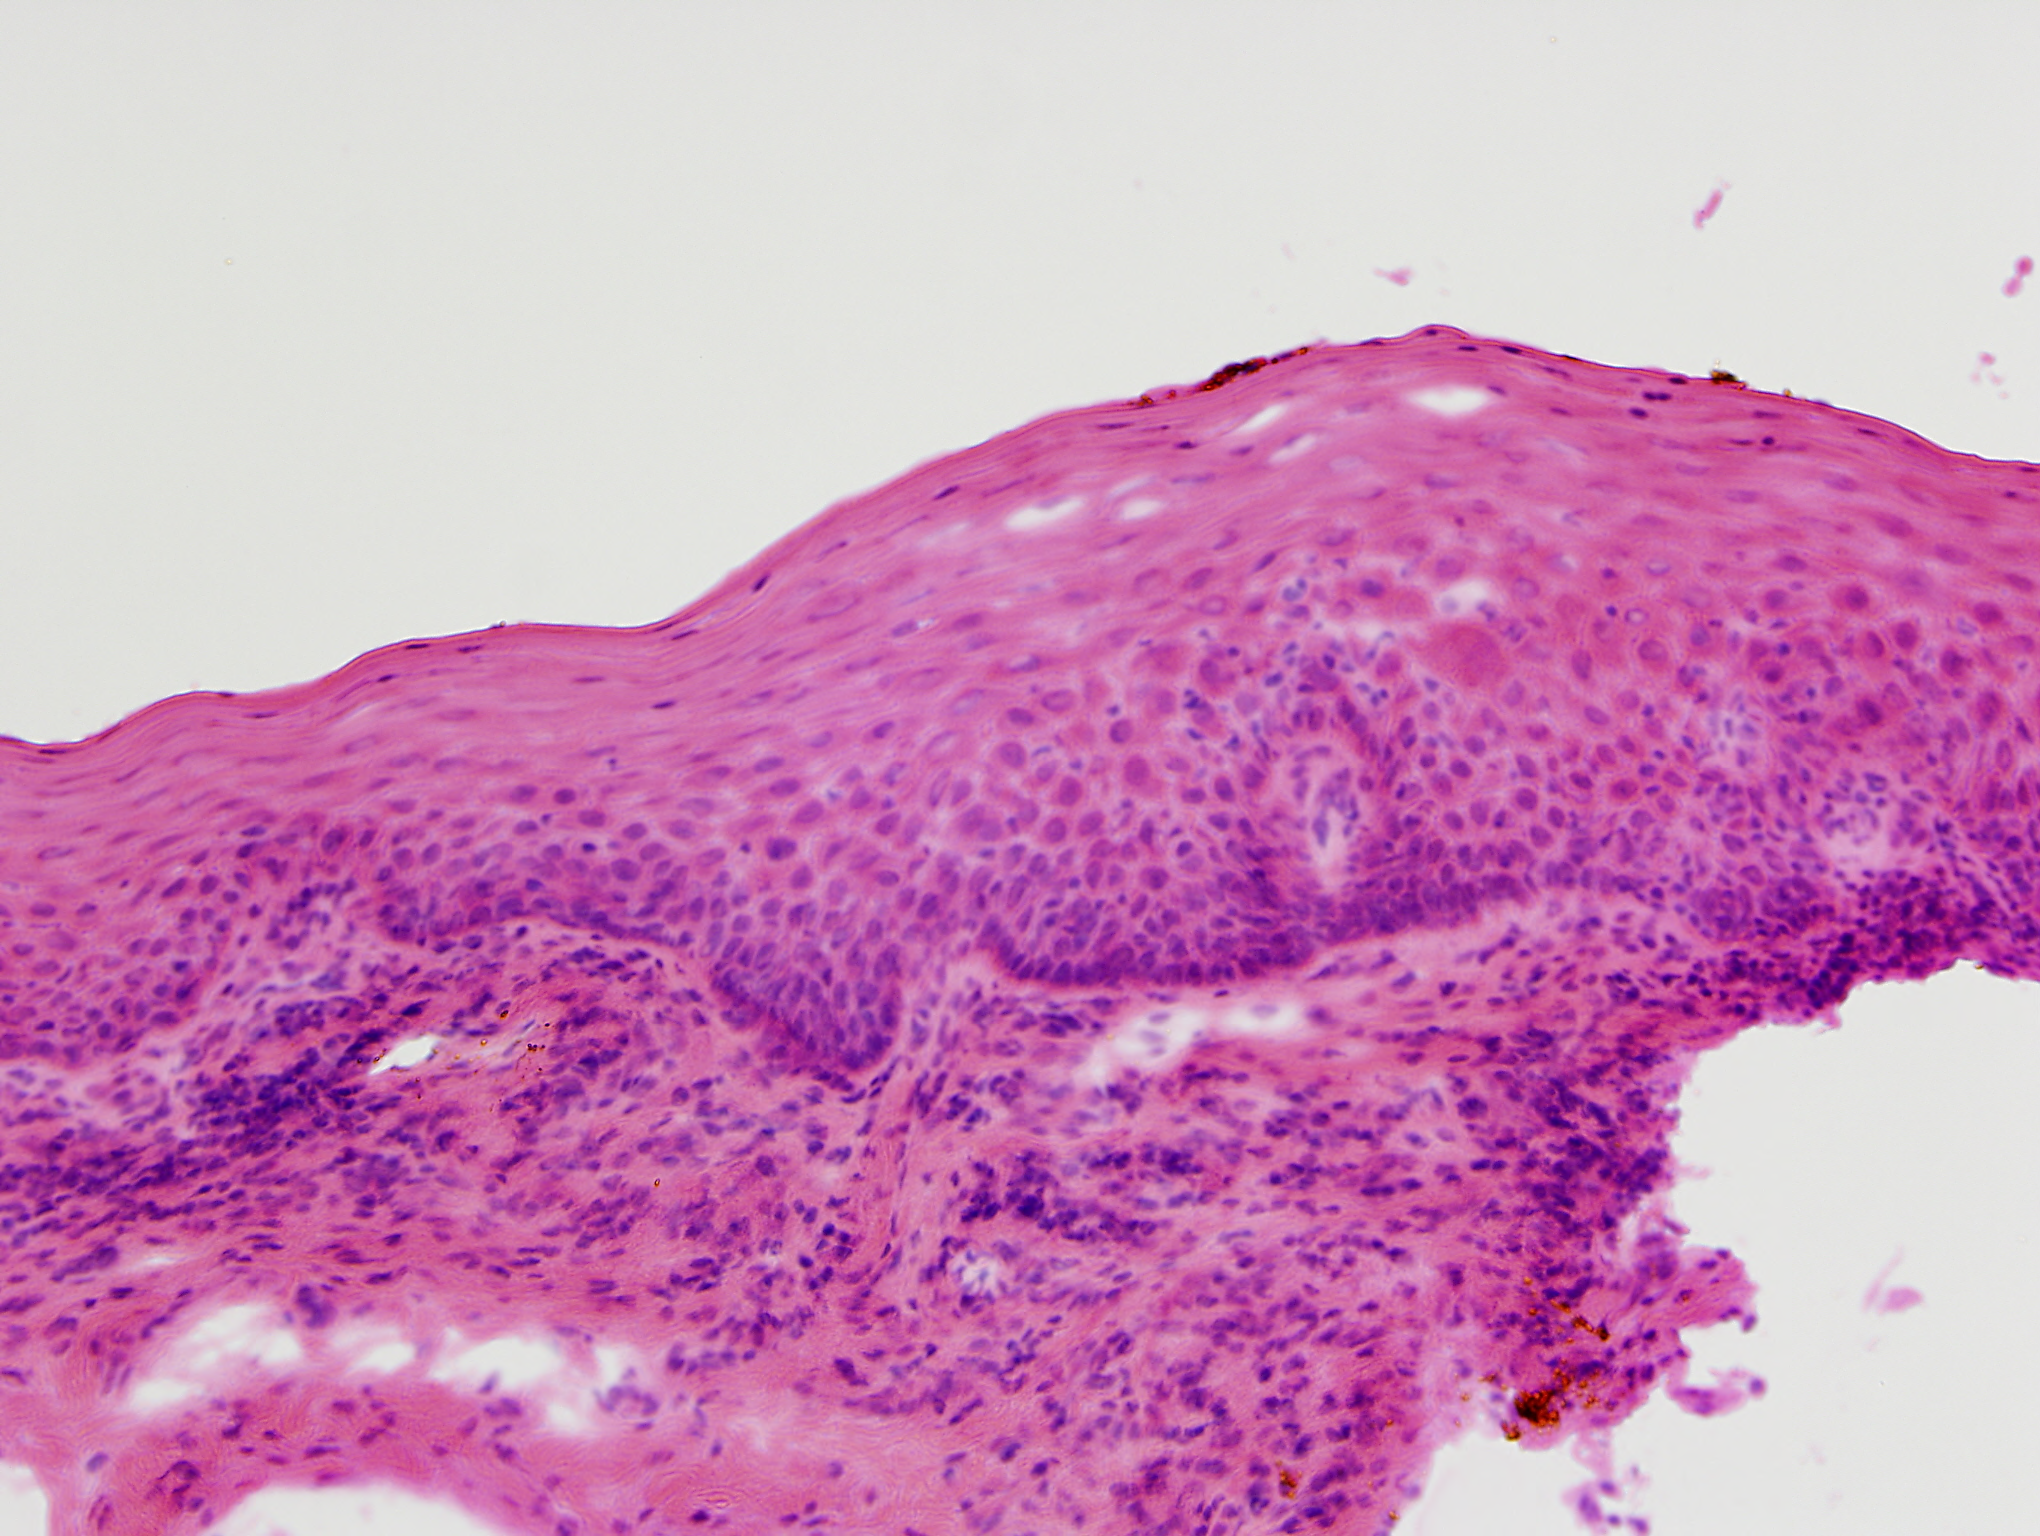
H&E-stained image of one small field of the section — roughly 1.0 x 0.8 mm in extent, frozen section from the top of the tissue portion, head and neck, solid tissue normal (non-tumour tissue) sample. Male patient; age at initial diagnosis 65 years. Inflammatory infiltration, as recorded: lymphocyte infiltration 10%, neutrophil infiltration 3%.
• this section: solid tissue normal (non-tumour) sample from the same patient
• patient diagnosis: Squamous cell carcinoma, NOS